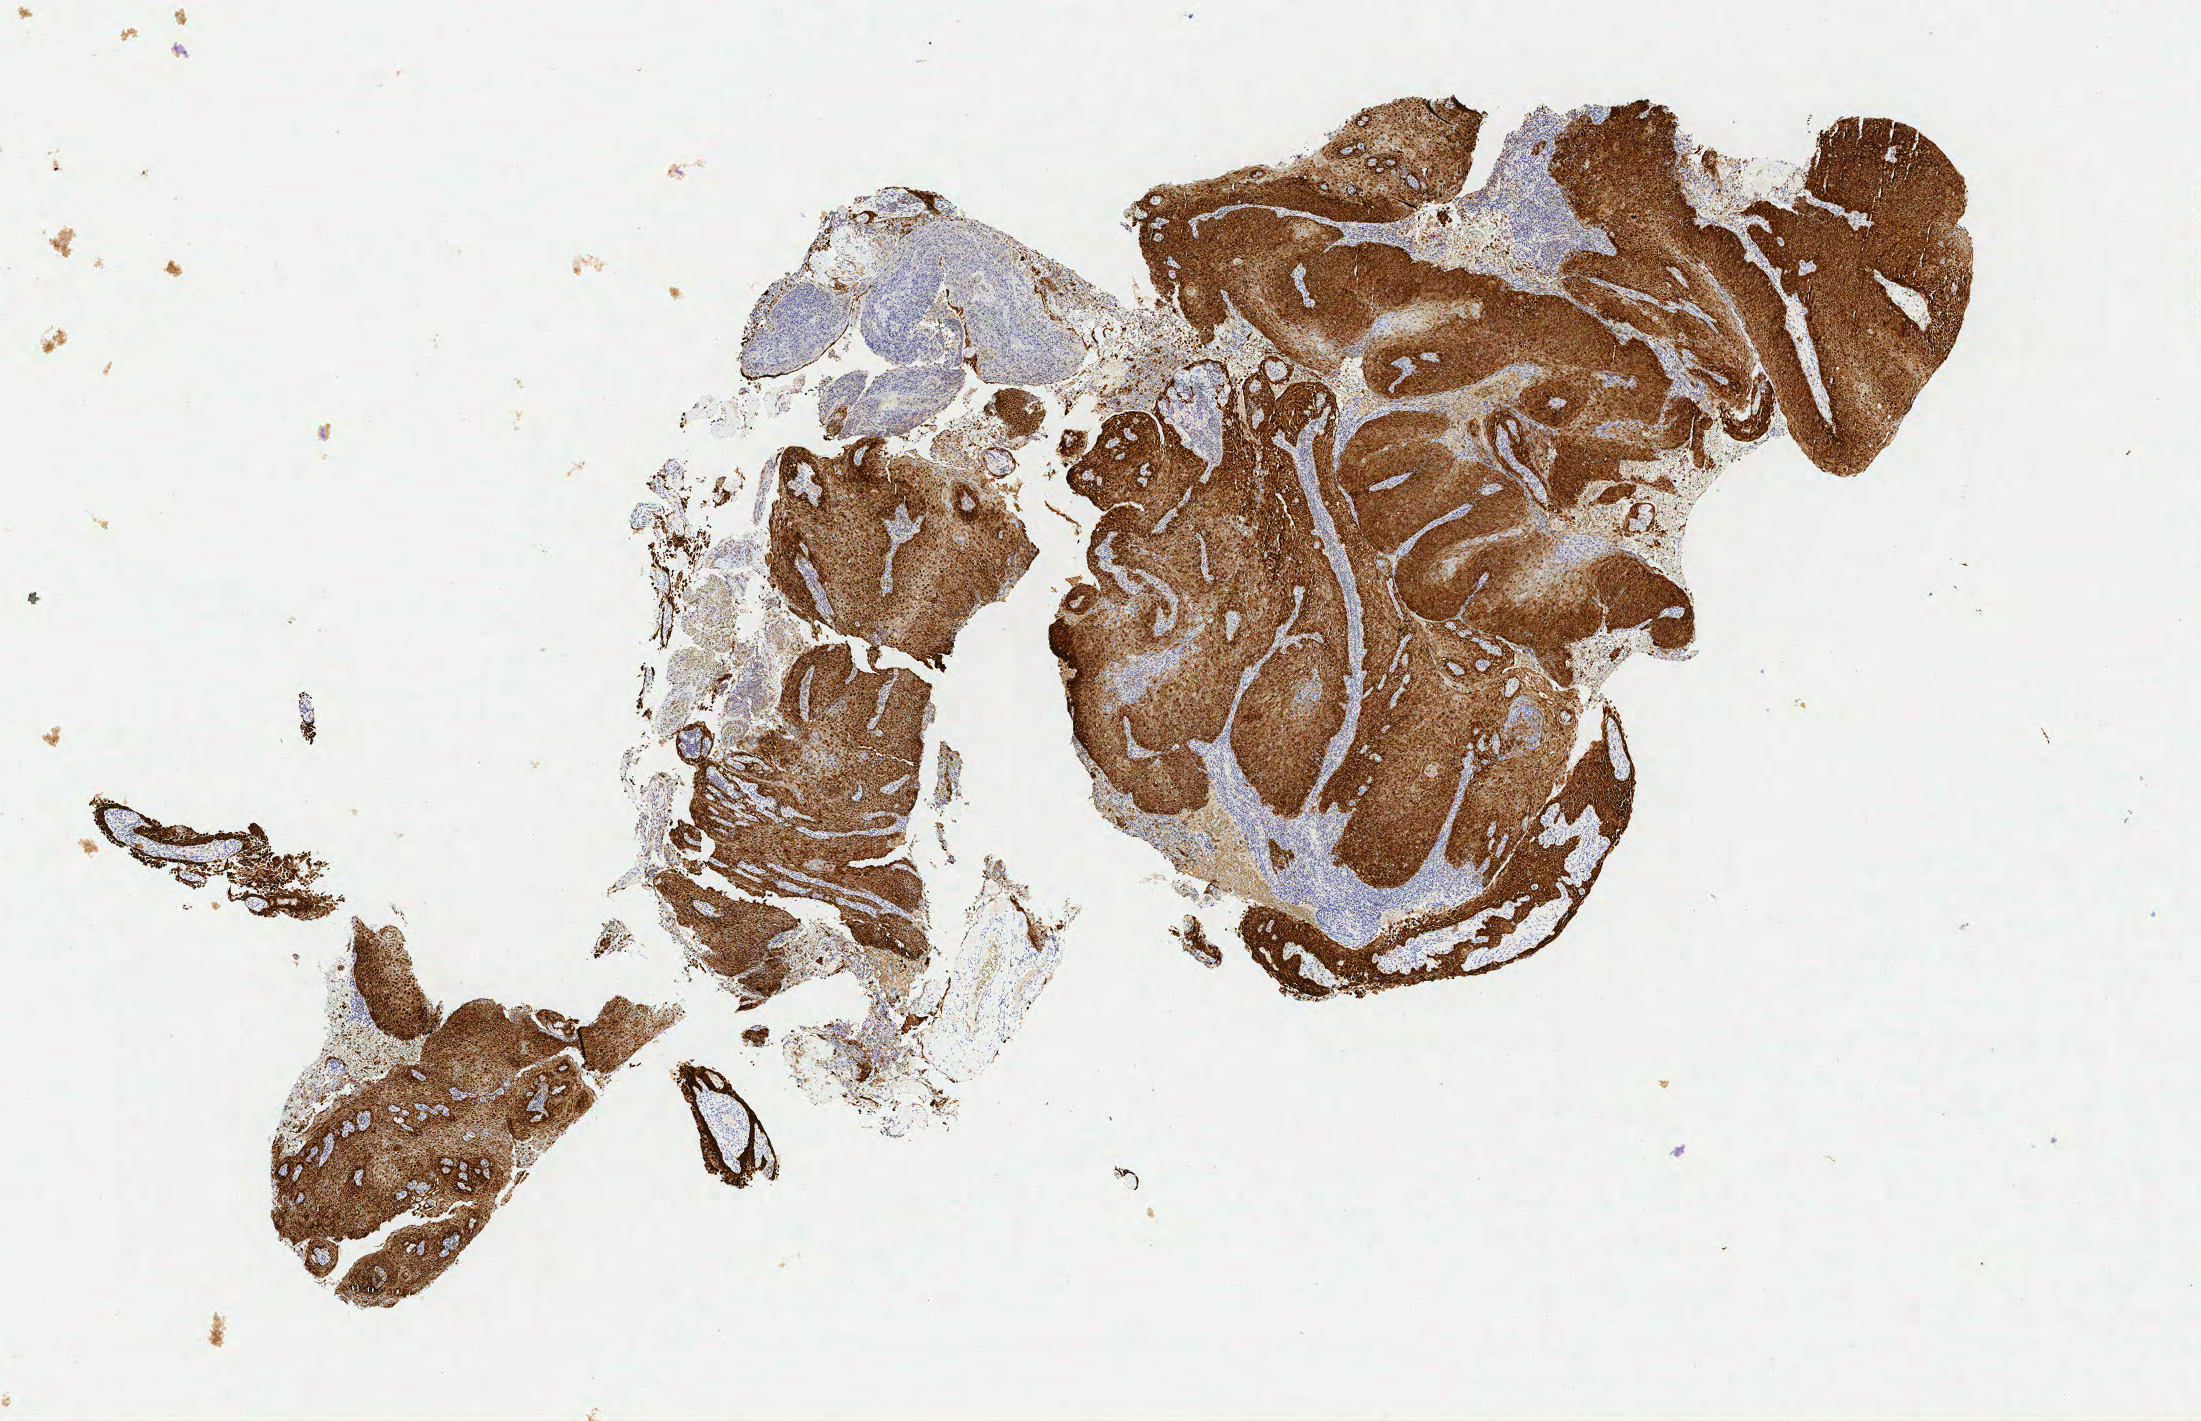
Immunohistochemistry (IHC) whole-slide image stained for p16 (p16INK4a), whole scanned area (about 8.7 x 5.6 mm) shown as a low-resolution overview. Tumor tissue. Site: cervix. Patient female; aged 47.
• histologic diagnosis: Squamous cell carcinoma, keratinizing, NOS